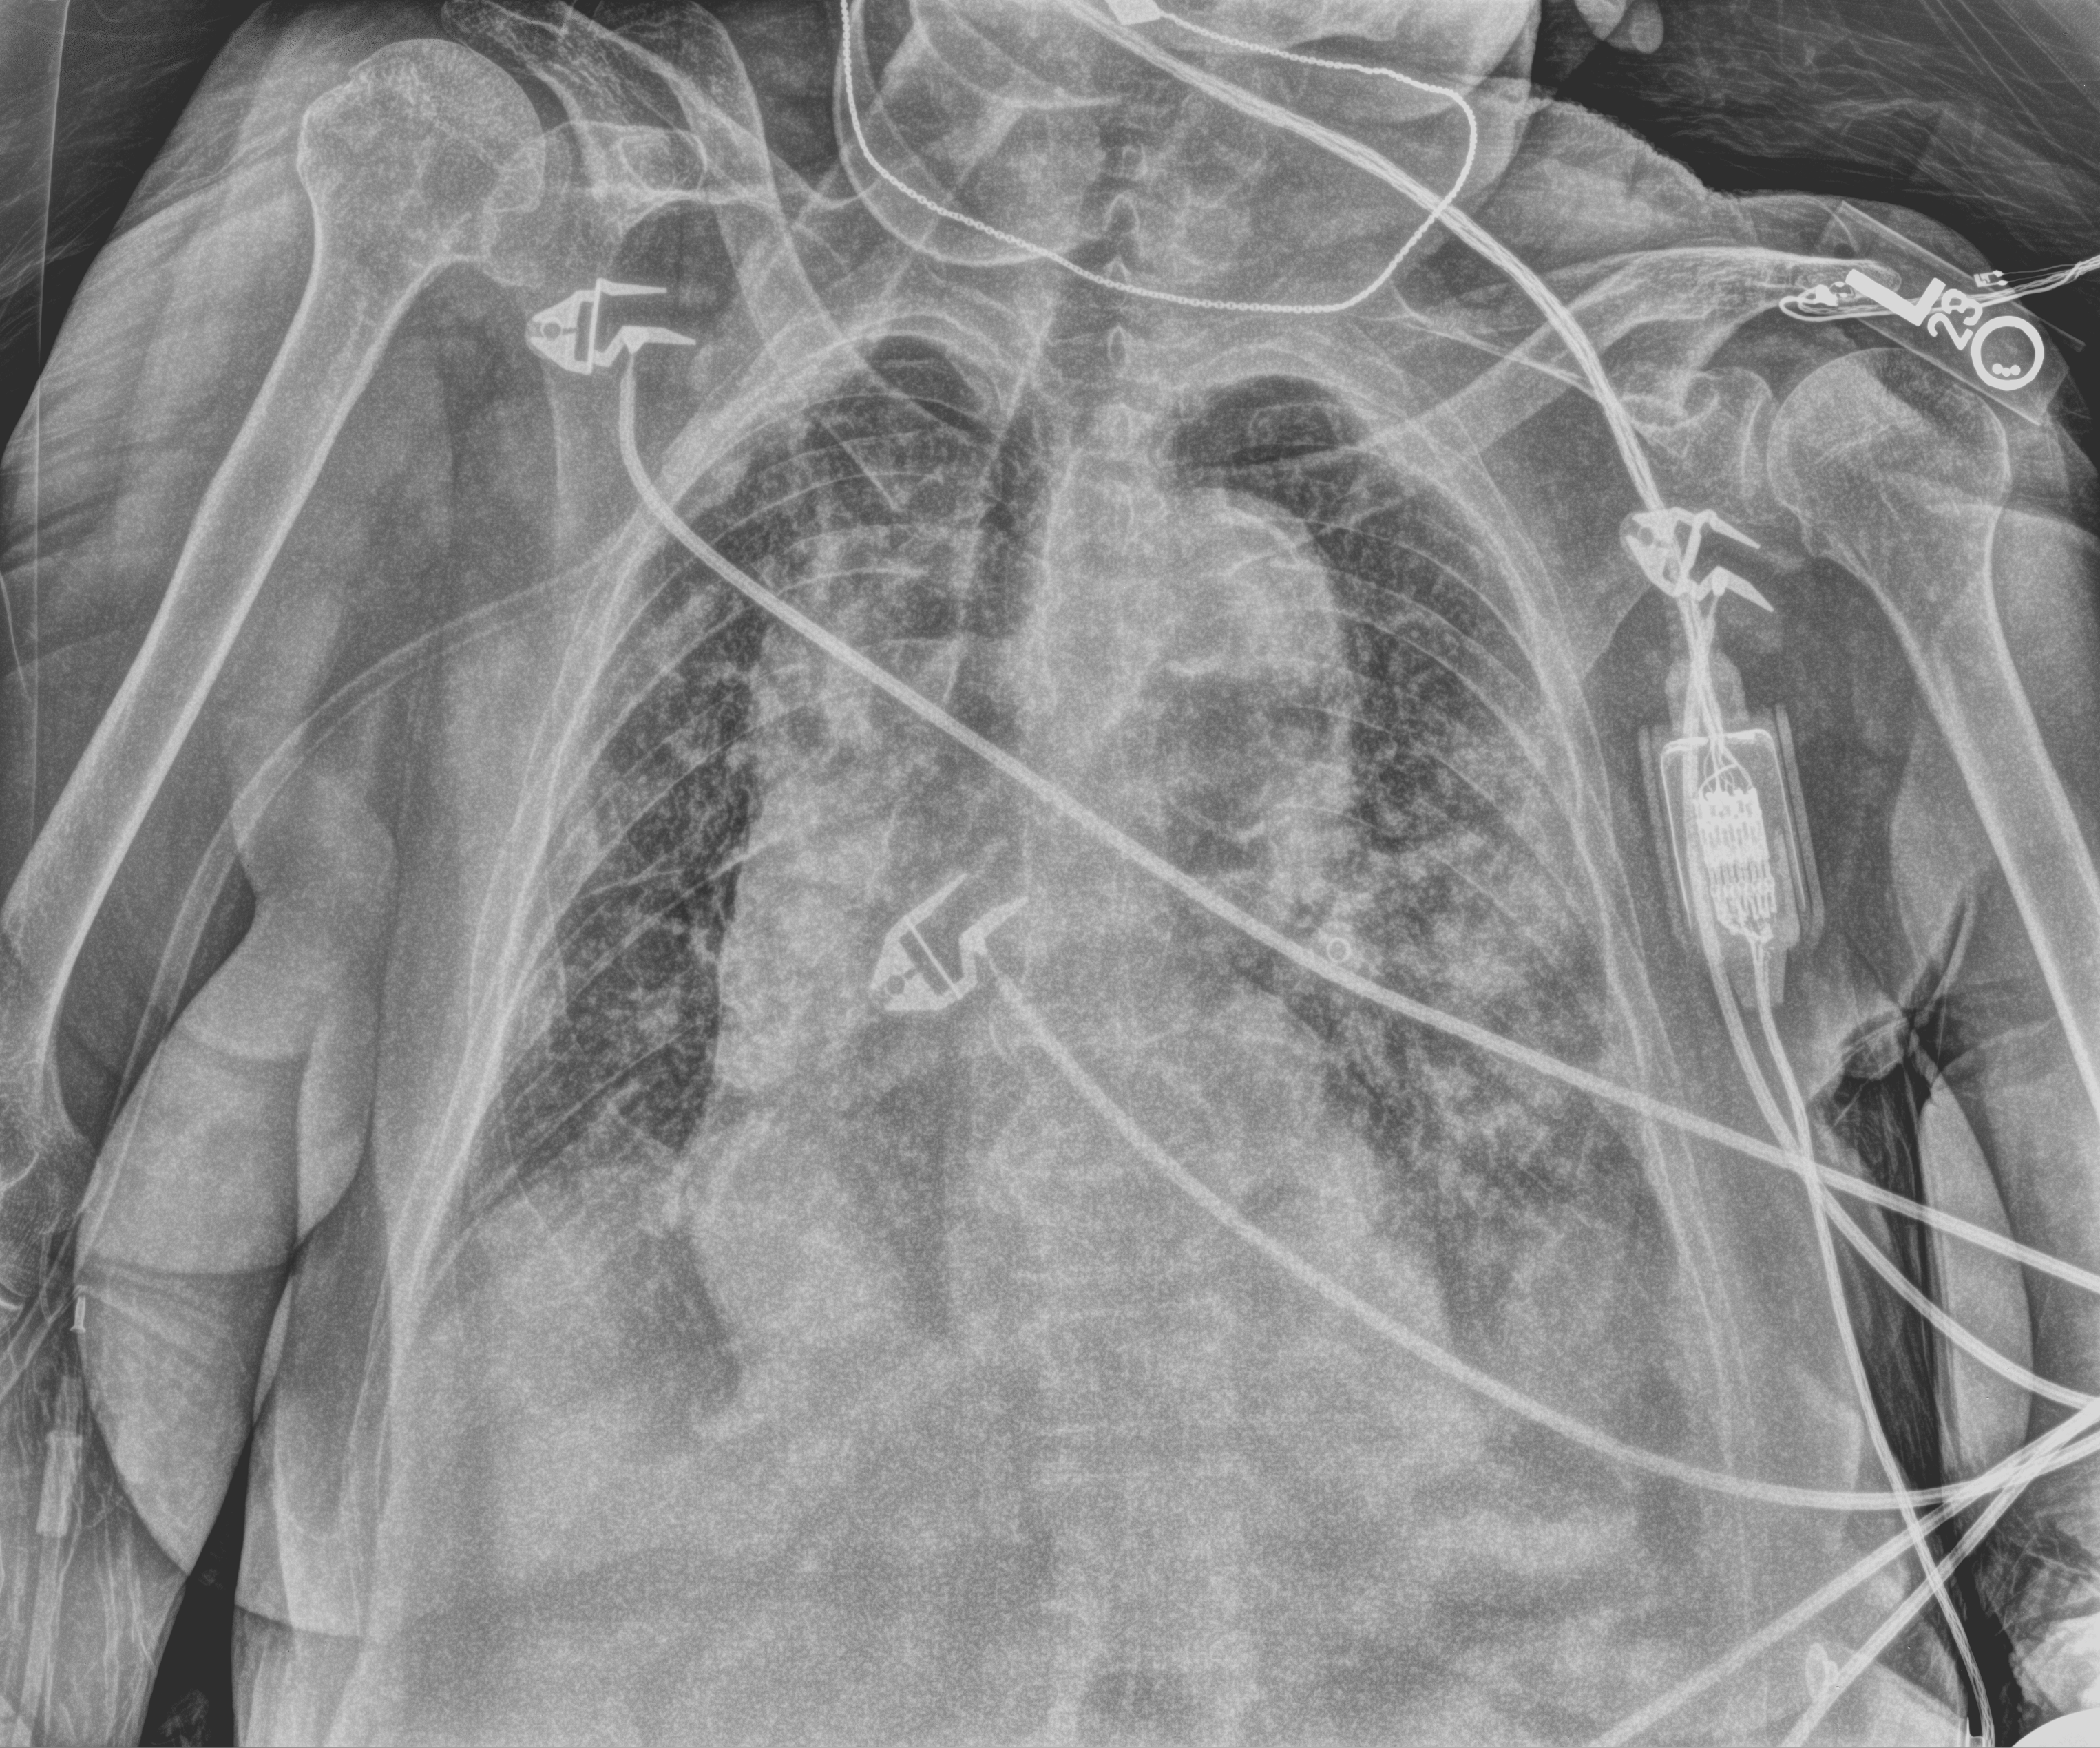
Chest X-ray (portable). Female patient hospitalised with COVID-19, age 75–90 years.
Admission-level facts for this patient (not findings on this image; timing relative to this image not recorded): COPD (admission record): no; smoking status (admission record): former.